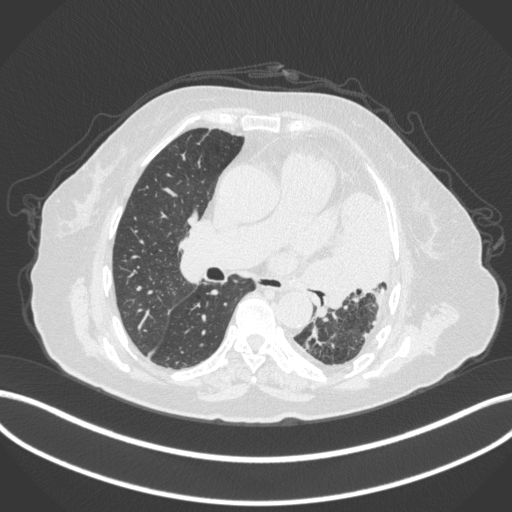
Chest CT, one axial slice; slice 203 of 399 in the series (ordered by position); 120 kVp; lung window (W 1500 / L -600 HU); 1 mm slice thickness; 512 × 512 image matrix, field of view 400 × 400 mm. Patient: female, 75 years. Case-level facts recorded for this patient, not image findings: clinical TNM (as recorded): T3 N3 M1.
Annotated regions visible in this slice (bounding box drawn by a radiologist):
- lung tumour (recorded histology: adenocarcinoma): bounding box <301,187,394,311> (left, top, right, bottom; pixels)